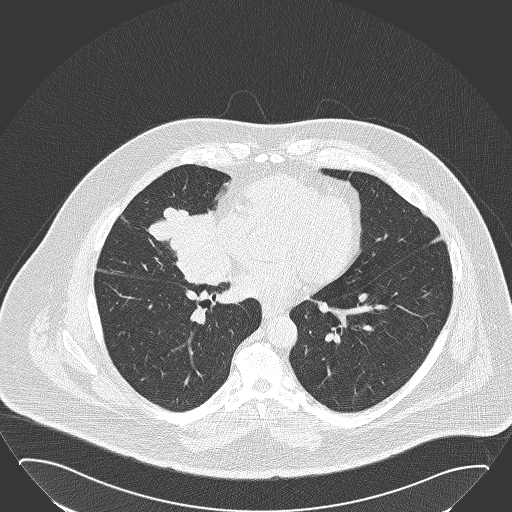
Low-dose screening chest CT, one axial slice; position 74 of 168 along the scan axis; 120 kVp; lung window (W 1500 / L -600 HU); 512 × 512 image matrix, field of view 432 × 432 mm.
Outlined on this slice (outlined manually by an expert reader):
- lesion 1 (tumor, hilum of right lung): bounding box [x1, y1, x2, y2] px = [147, 207, 230, 286]